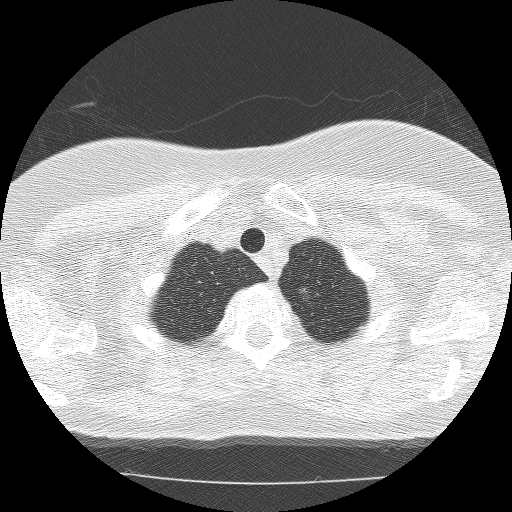
Chest CT (low-dose screening protocol), one axial image, second screening round (one year after baseline), lung window (W 1500 / L -600 HU), 2.5 mm slice thickness, lung (sharp) reconstruction kernel (BONE), slice 14 of 120 in the series. Female participant, aged 59 years at enrolment. Former smoker at enrolment.
Expert-annotated lung lesion, bounding box <281,278,324,315> (left, top, right, bottom; pixels). The screening reader recorded 3 non-calcified nodules or masses ≥4 mm on this exam (right upper lobe, left upper lobe, right upper lobe); which of them this box marks is not recorded. Lung cancer was diagnosed 419 days after this screen (after the third annual screen): bronchiolo-alveolar adenocarcinoma, NOS, left upper lobe, well differentiated (G1), stage IA (AJCC 6th edition), 10 mm at pathology.